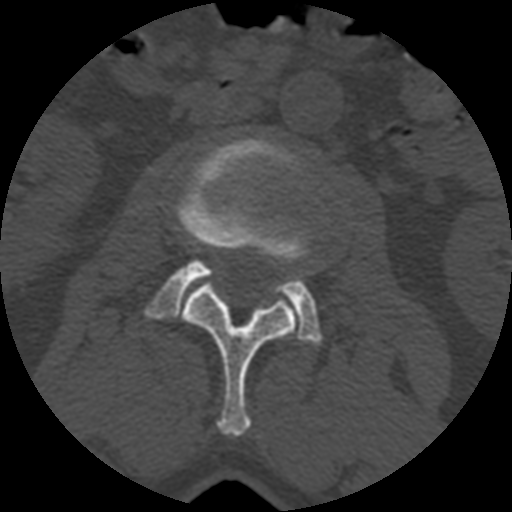
CT including the spine, one axial slice. Slice 322 of 399 in the series (ordered by position). Reconstruction kernel STANDARD. 120 kVp. Bone window (W 1800 / L 400 HU). 1.25 mm slice thickness. 512 × 512 image matrix. Patient age 71 years. From the clinical record (not read from this slice): primary cancer: prostate.
Outlined on this slice (semi-automatically segmented with operator editing):
- L2 vertebra: bounding box (x1, y1, x2, y2) in pixels: (175, 282, 295, 436)
- L3 vertebra: (144, 138, 322, 344)